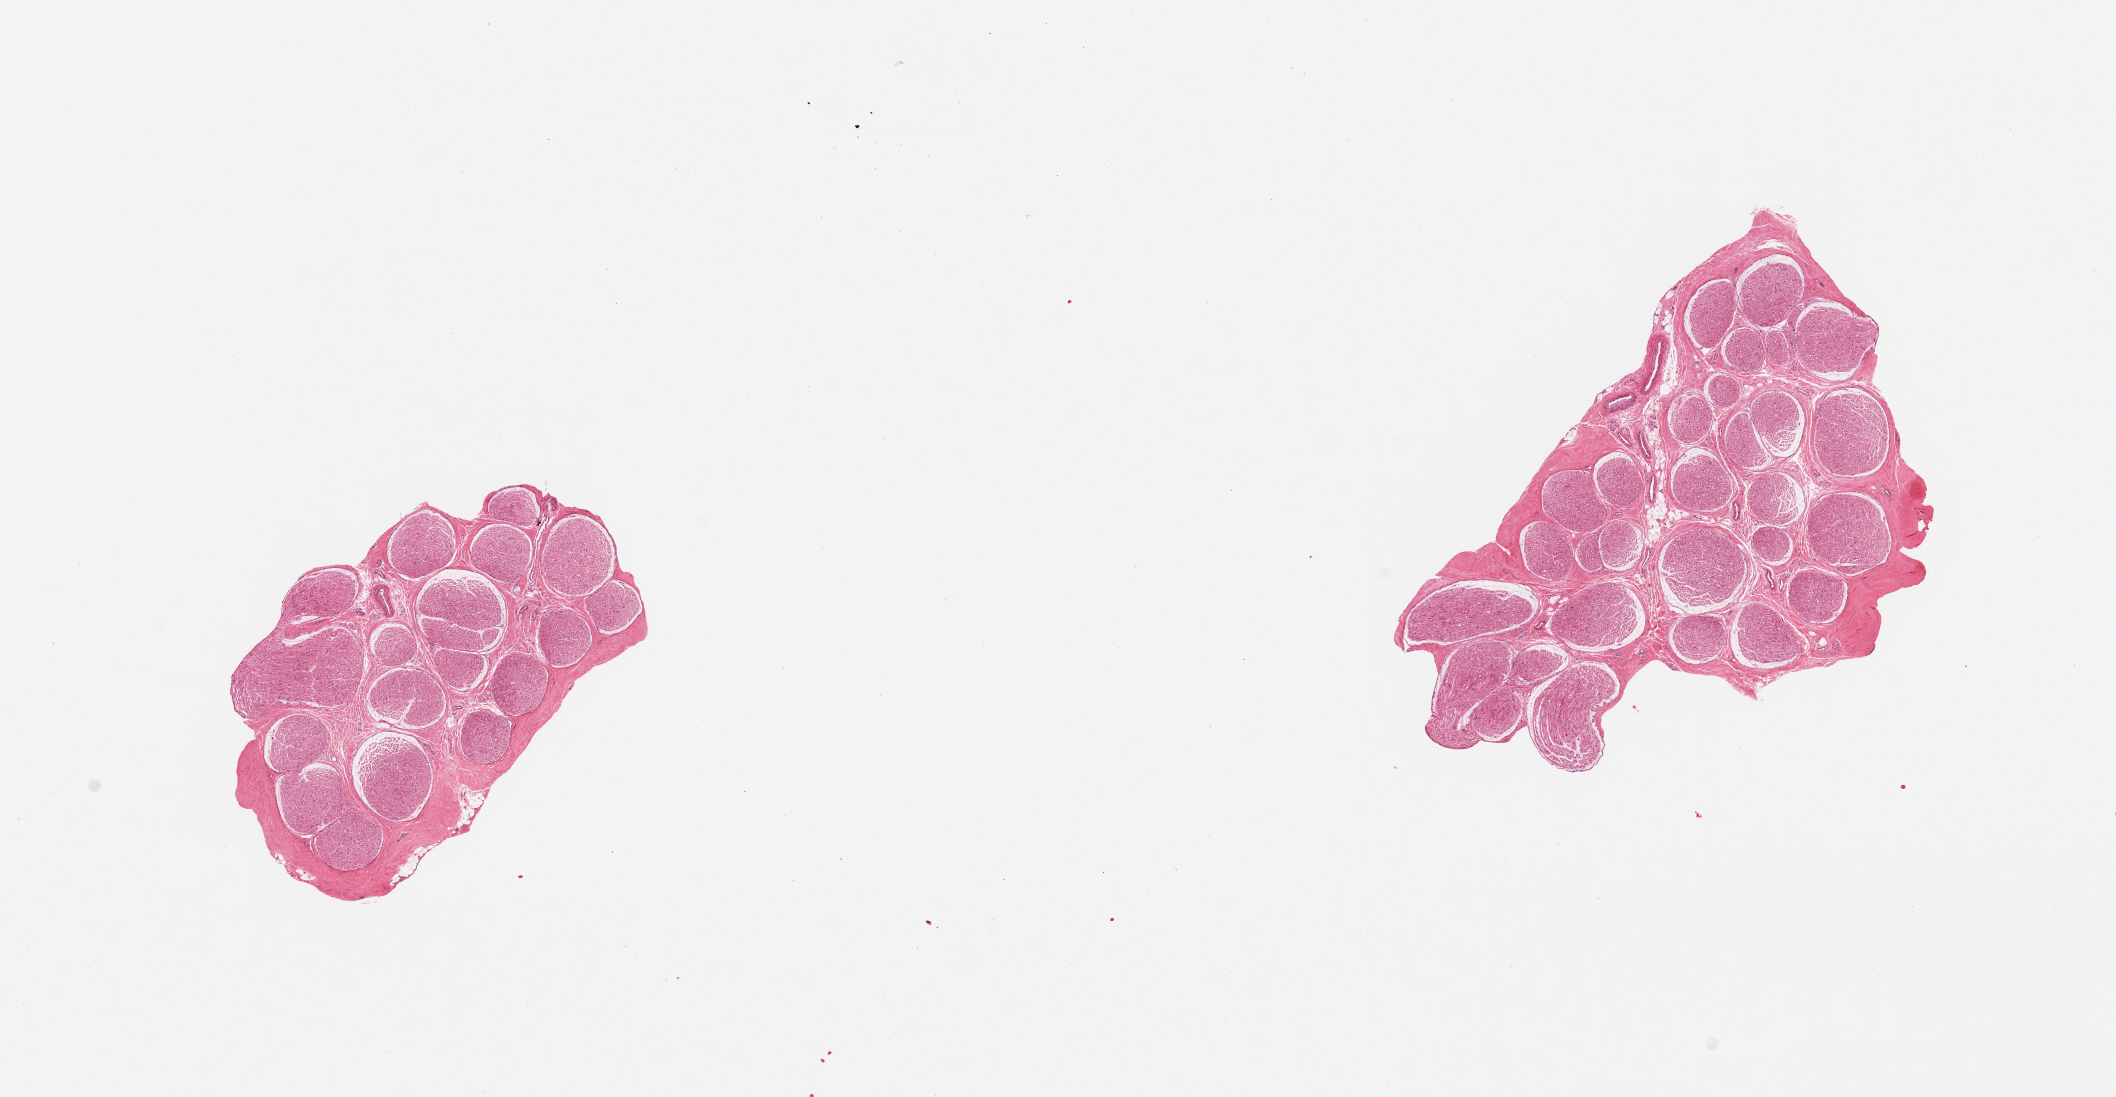
Whole-slide image, haematoxylin and eosin stain, brightfield — shown as a low-resolution overview of the whole scanned area (about 16.7 x 8.7 mm). PAXgene-fixed, paraffin-embedded tissue. Section of tibial nerve (target tissue). Tissue donor sample. Female donor.
Review note (as recorded): 2 pieces; well trimmed.